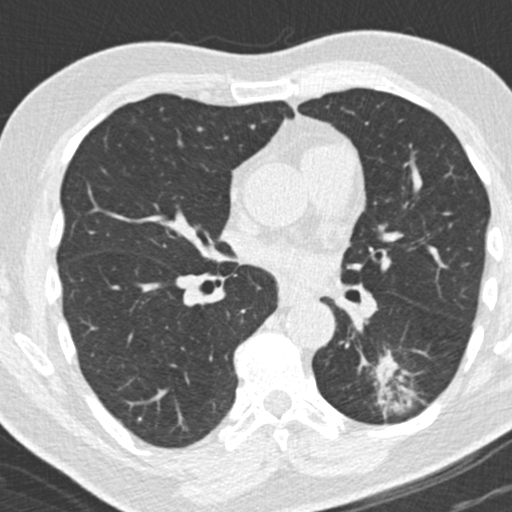
Axial slice from a low-dose chest CT screening exam. Third screening round (two years after baseline). Lung window (W 1500 / L -600 HU). Standard (soft-tissue) reconstruction kernel (B30f). 120 kVp. Slice 81 of 180 in the series. 512 × 512 image matrix, field of view 300 × 300 mm. Male, age 66 years at enrolment. Former smoker at enrolment.
Expert-annotated lung lesion, bounding box <357,354,425,426> (left, top, right, bottom; pixels). Screening reader's record for this exam (one nodule recorded; not confirmed to be the boxed lesion): non-calcified nodule or mass ≥4 mm, left lower lobe, 31 × 24 mm, spiculated (stellate) margins, pre-existing on the prior screen: yes; interval growth: yes. Official screen result: positive, other. Later outcome: lung cancer diagnosed 56 days after this screen — adenocarcinoma, NOS, left lower lobe, poorly differentiated (G3), stage IB (AJCC 6th edition), 38 mm at pathology.